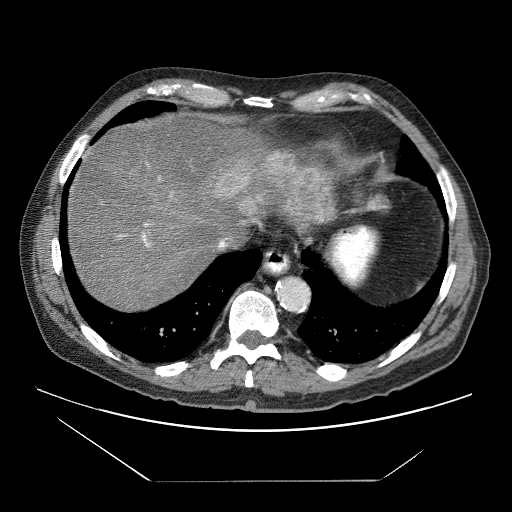
Contrast-enhanced abdominal CT (liver protocol), one axial slice; position 63 of 83 along the scan axis; reconstruction kernel STANDARD; soft-tissue window (W 400 / L 40 HU); 2.5 mm slice thickness; 512 × 512 image matrix, field of view 420 × 420 mm. From the clinical record (not read from this slice): diagnosis: hepatocellular carcinoma (patient treated with transarterial chemoembolisation; whether this scan precedes or follows treatment is not stated here); TNM stage (as recorded): Stage-IVB; Child-Pugh class: B; tumour differentiation: poorly differentiated.
Outlined on this slice (semi-automatic segmentation, software-assisted and operator-edited):
- liver parenchyma outside the tumour (the mass and vessels are separate outlines, so this box may not span the whole liver): box from (x=68, y=119) to (x=336, y=308) px
- mass: (x=212, y=152)–(x=334, y=228)
- liver vessels: (x=84, y=155)–(x=323, y=248)